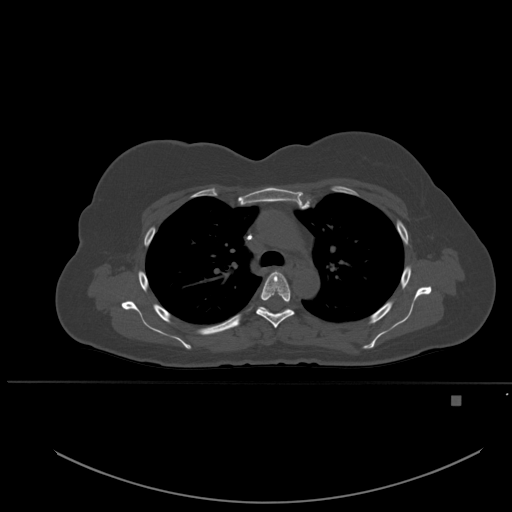
CT including the spine, one axial slice; position 378 of 651 along the scan axis; bone window (W 1800 / L 400 HU); 1.5 mm slice thickness; 512 × 512 image matrix, field of view 443 × 443 mm. Patient: female, 49 years. Case-level facts recorded for this patient, not image findings: primary cancer: breast; vertebrae with lytic lesions (as recorded): L3, T12, L4.
Annotated regions visible in this slice (semi-automatic segmentation, software-assisted and operator-edited):
- T4 vertebra: bounding box [x1, y1, x2, y2] px = [256, 271, 294, 328]
- T5 vertebra: [233, 307, 292, 328]